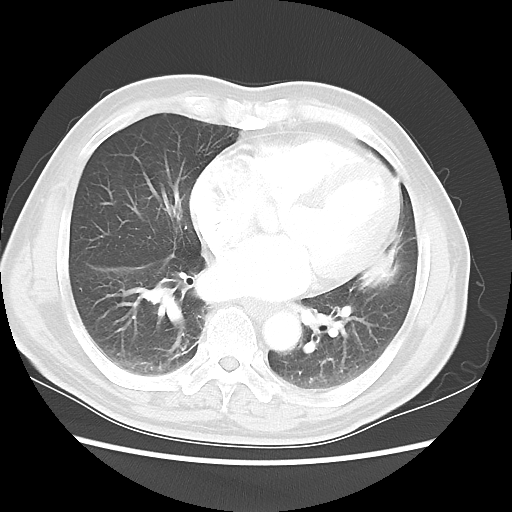
Chest CT, one axial slice. Slice 19 of 50 in the series (ordered by position). 120 kVp. Lung window (W 1500 / L -600 HU). 512 × 512 image matrix, field of view 360 × 360 mm. Male patient, age 69 years. From the clinical record (not read from this slice): clinical TNM (as recorded): T3 N1 M1a.
Structures marked on this image (rectangle marked by the reading radiologist):
- lung tumour (recorded histology: squamous cell carcinoma): bounding box <342,235,400,298> (left, top, right, bottom; pixels)